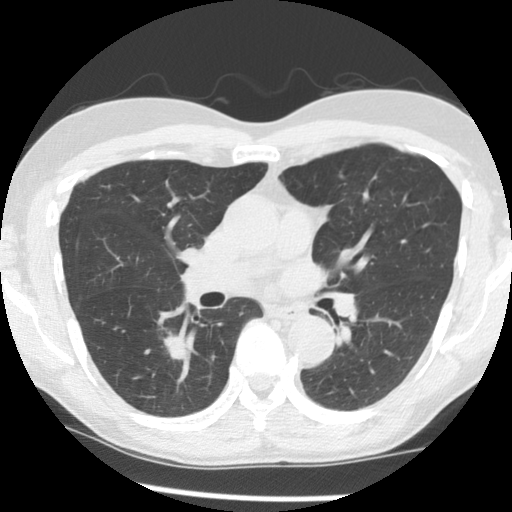
Low-dose screening chest CT, one axial slice; position 79 of 145 along the scan axis; 140 kVp; lung window (W 1500 / L -600 HU); 2.5 mm slice thickness; 512 × 512 image matrix.
Annotated regions visible in this slice (expert manual segmentation):
- lesion 1 (tumor, lower lobe of right lung): bounding box (x1, y1, x2, y2) in pixels: (164, 334, 187, 360)